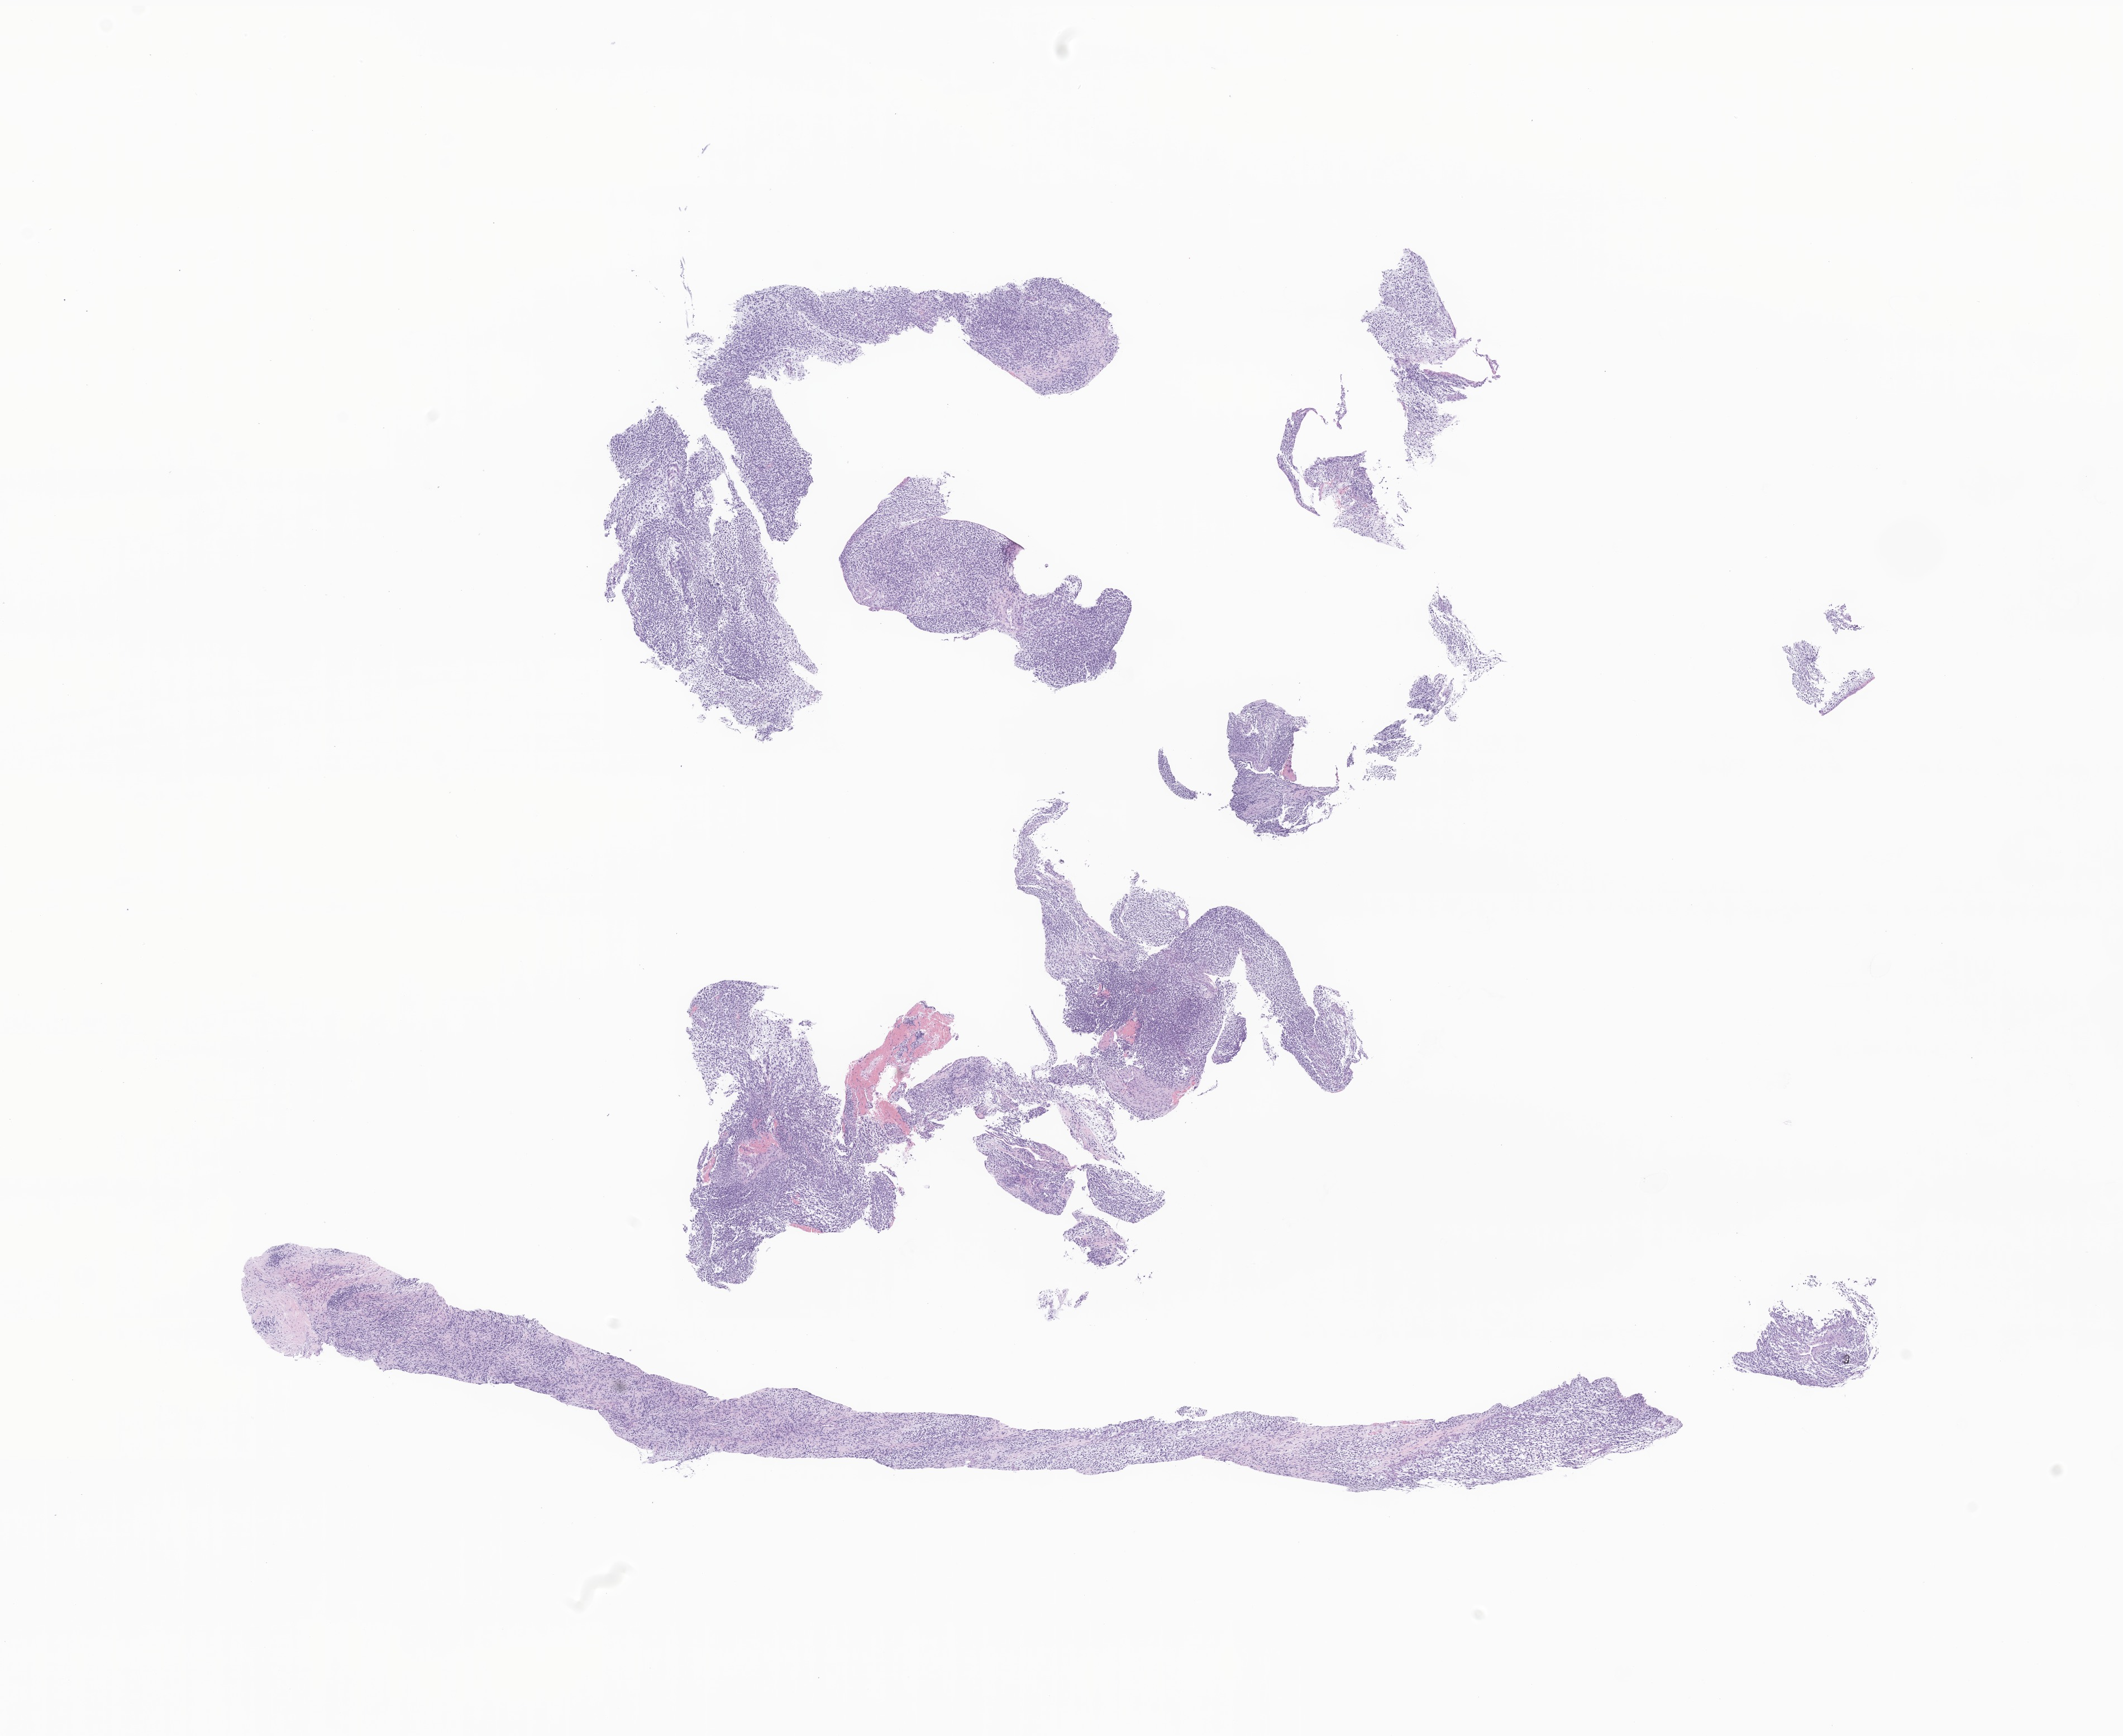
Digitized haematoxylin and eosin-stained section of tumor tissue from the soft tissue of pelvis, whole scanned area (about 16.0 x 13.1 mm) shown as a low-resolution overview, formalin-fixed paraffin-embedded section. Patient: male, age 34 months (2 years 10 months).
Recorded diagnosis: Embryonal rhabdomyosarcoma, NOS.